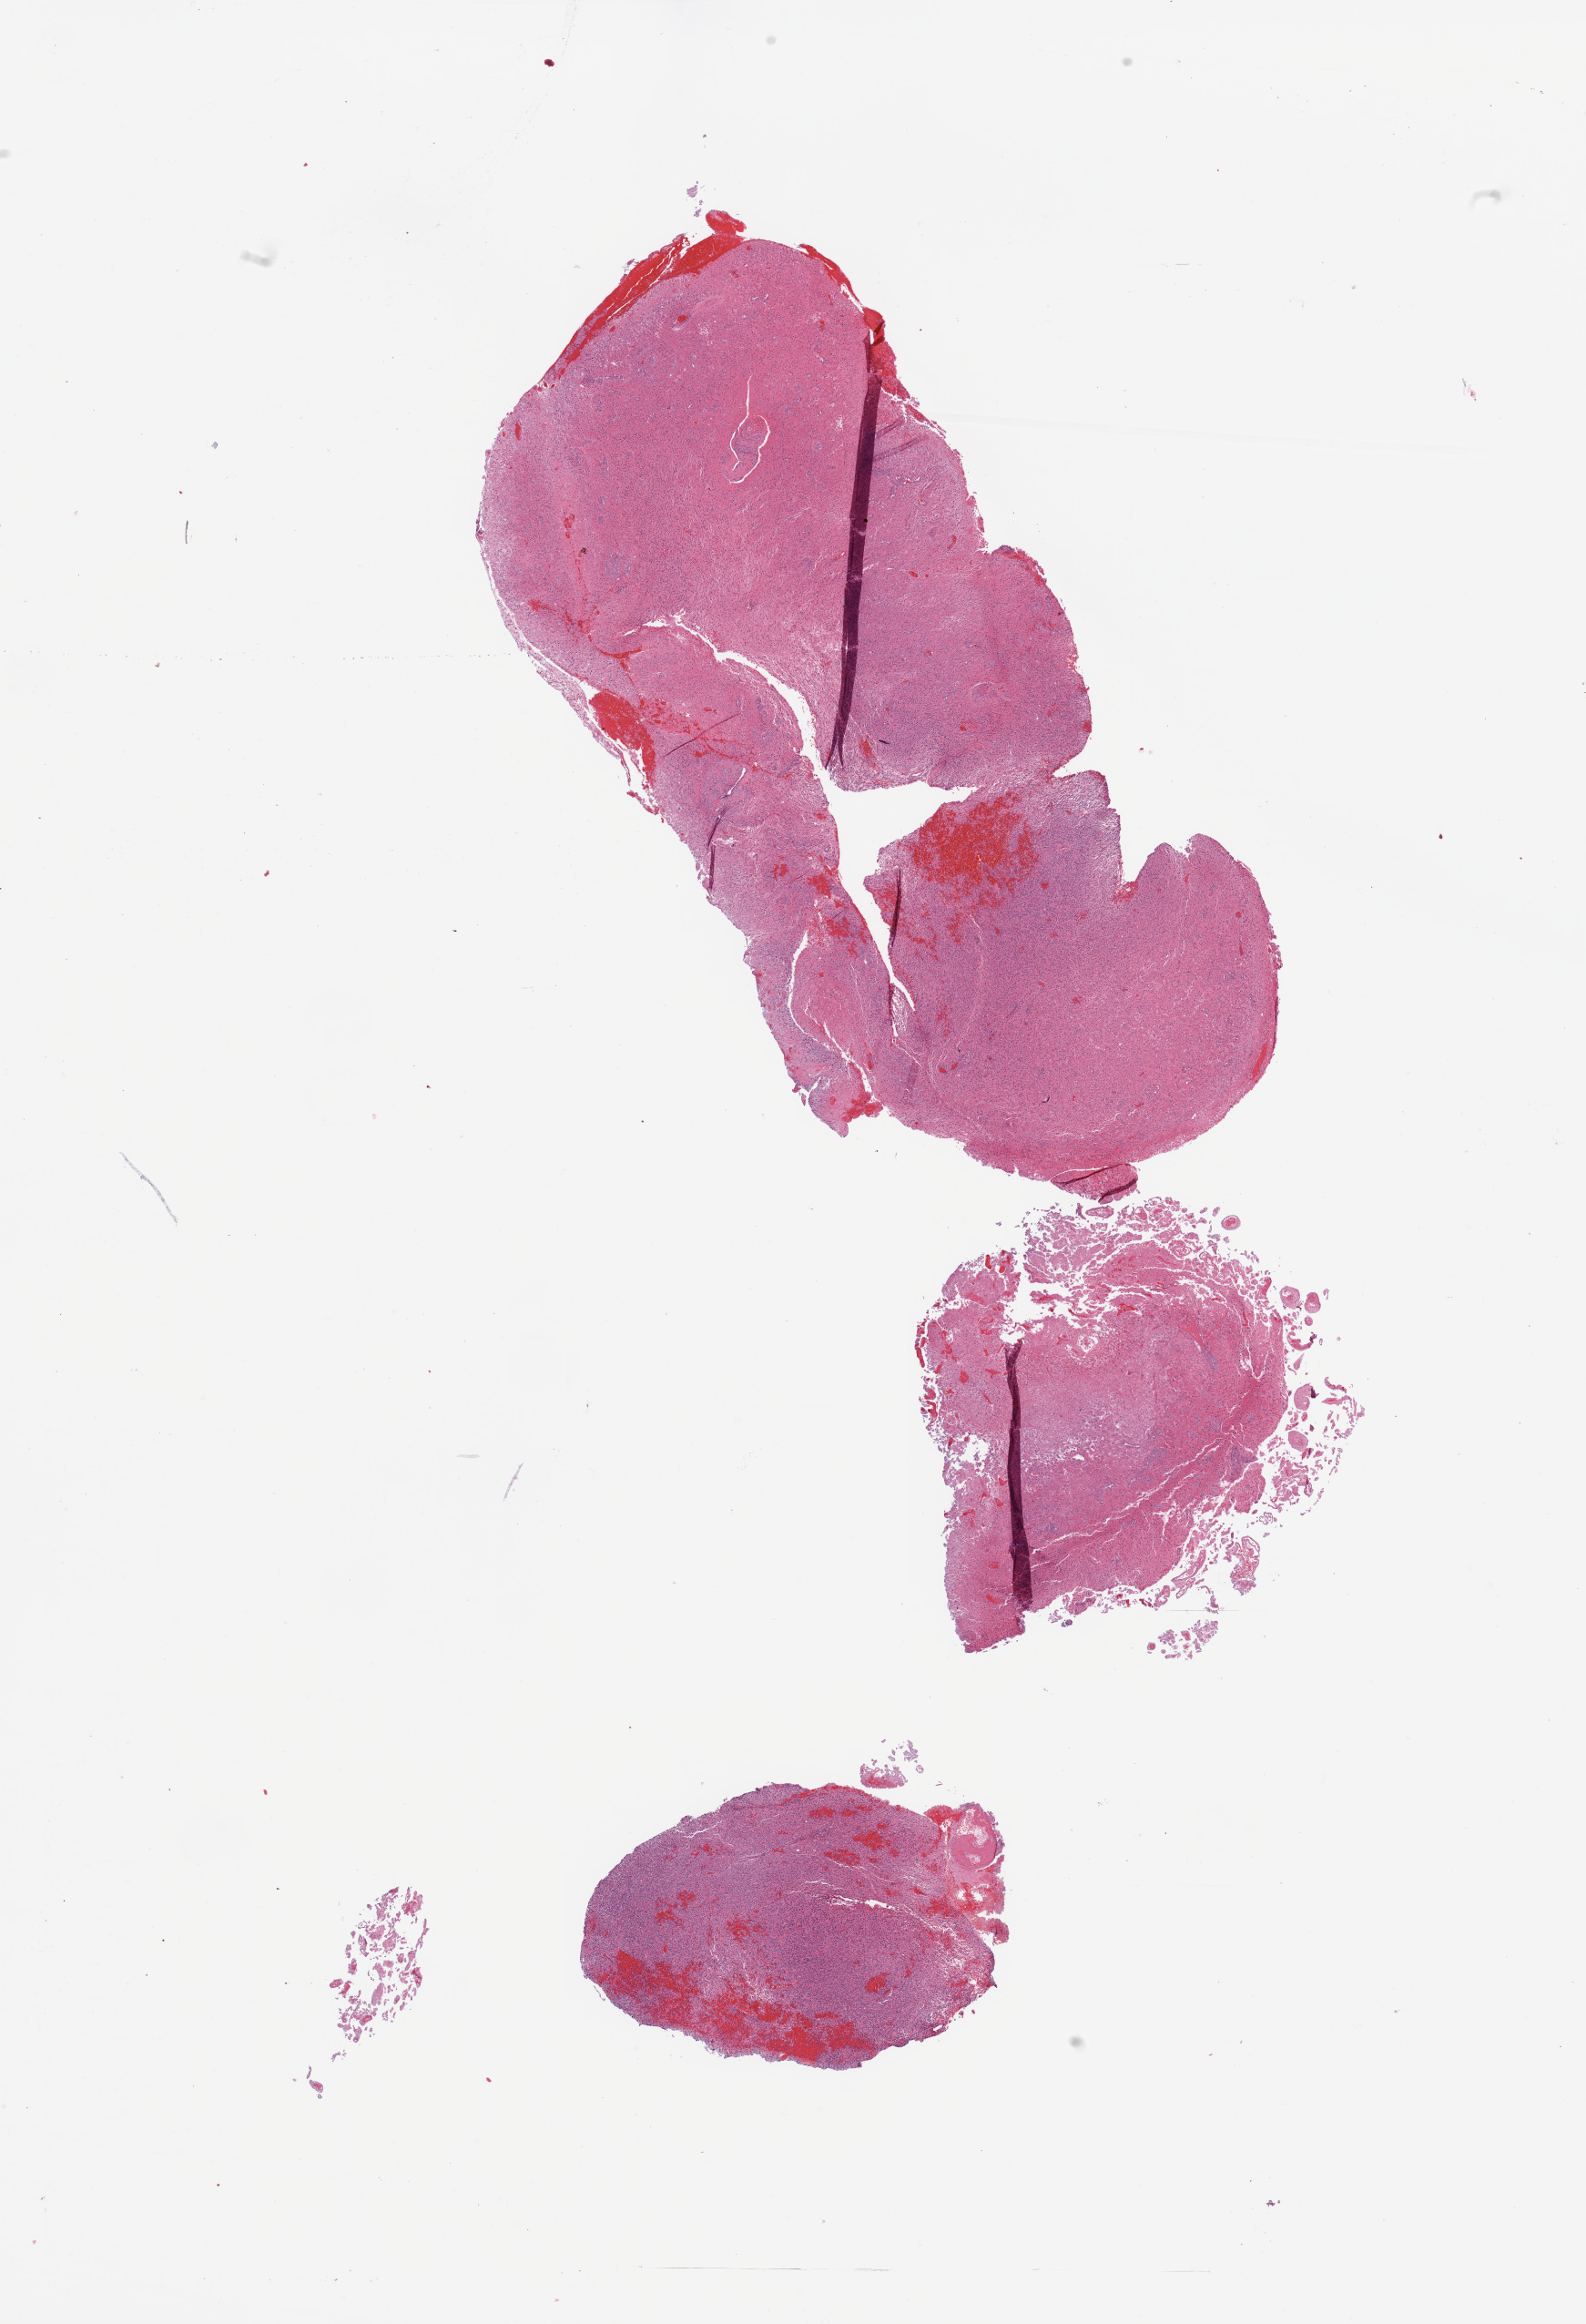
Digitized Hematoxylin and eosin (H&E) stained tissue section (whole slide), whole scanned area (about 13.8 x 20.2 mm, slide scanned at 20x) shown as a low-resolution overview. Tumour tissue sample, sampled site: frontal lobe. 54-year-old male patient. Composition of this section per pathologist review: tumour nuclei 80%, necrosis 5%.
Primary tumour site (as recorded): frontal lobe. Histologic diagnosis: Glioblastoma.